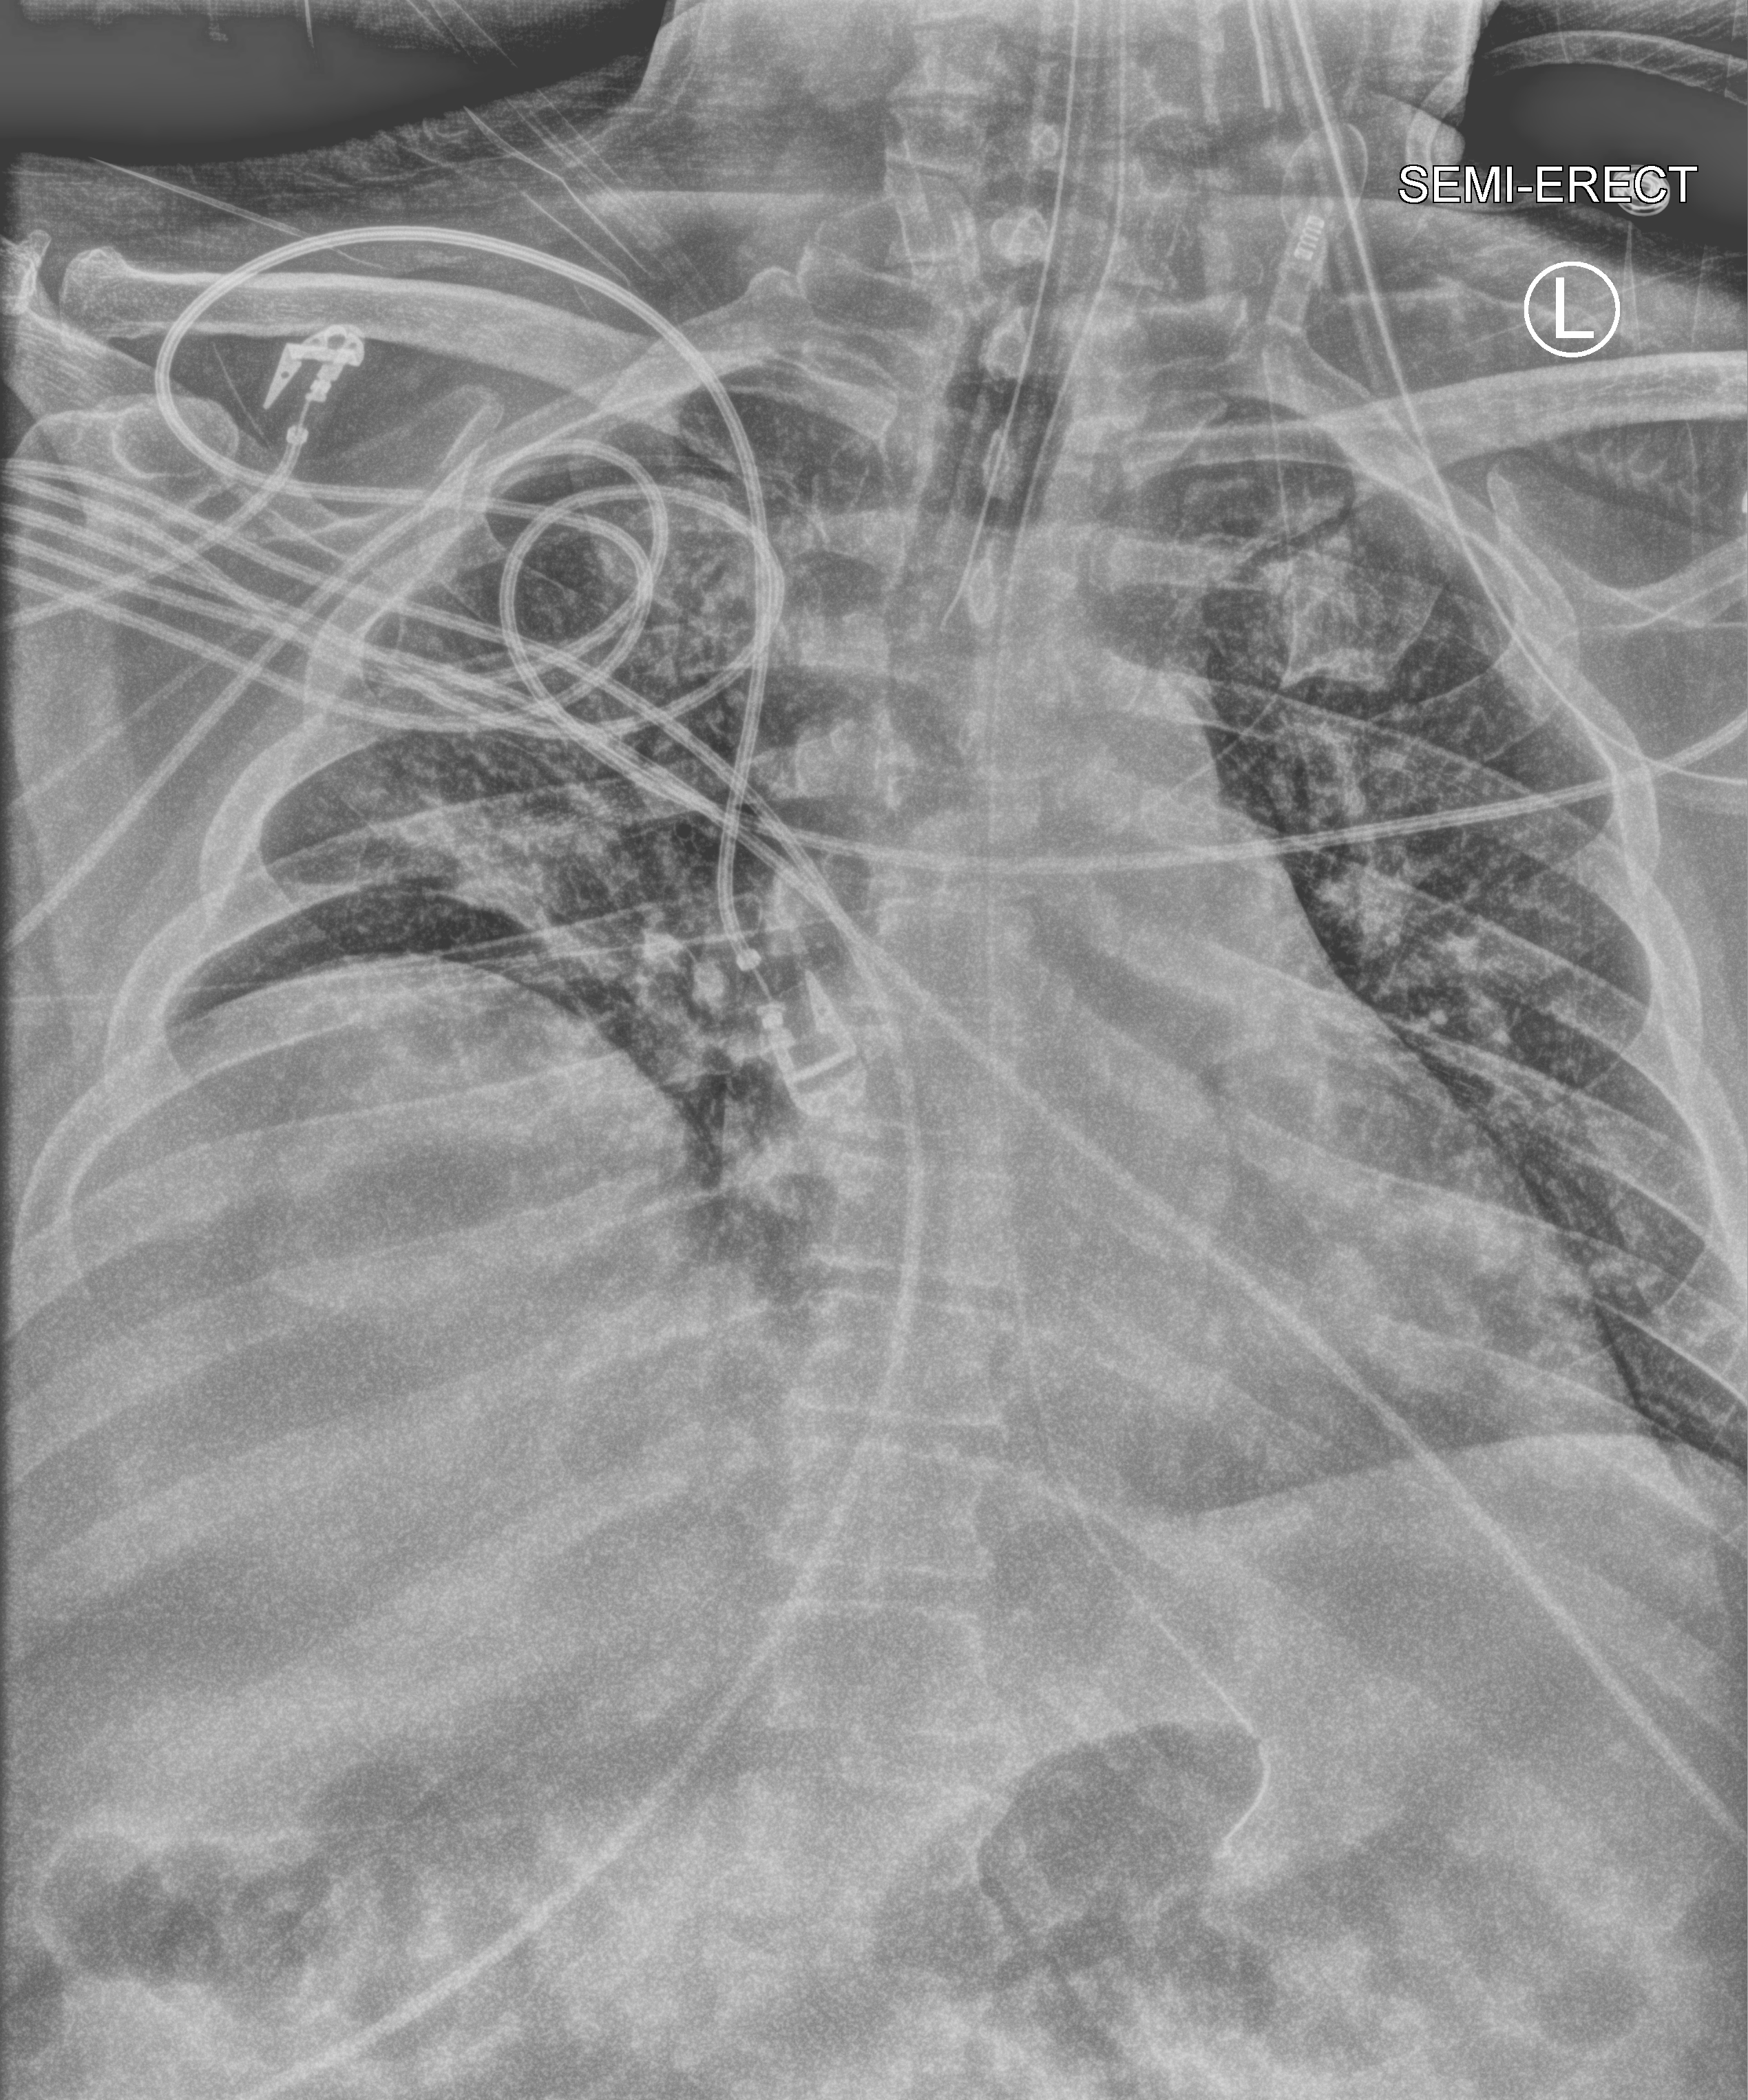
Chest X-ray (portable); anteroposterior (AP) projection. Patient hospitalised with COVID-19; male, aged 18–59 years.
Hospital-stay facts (about this admission, not read from this image; timing relative to this image not recorded): chronic kidney disease (admission record): no; hypertension (admission record): yes.